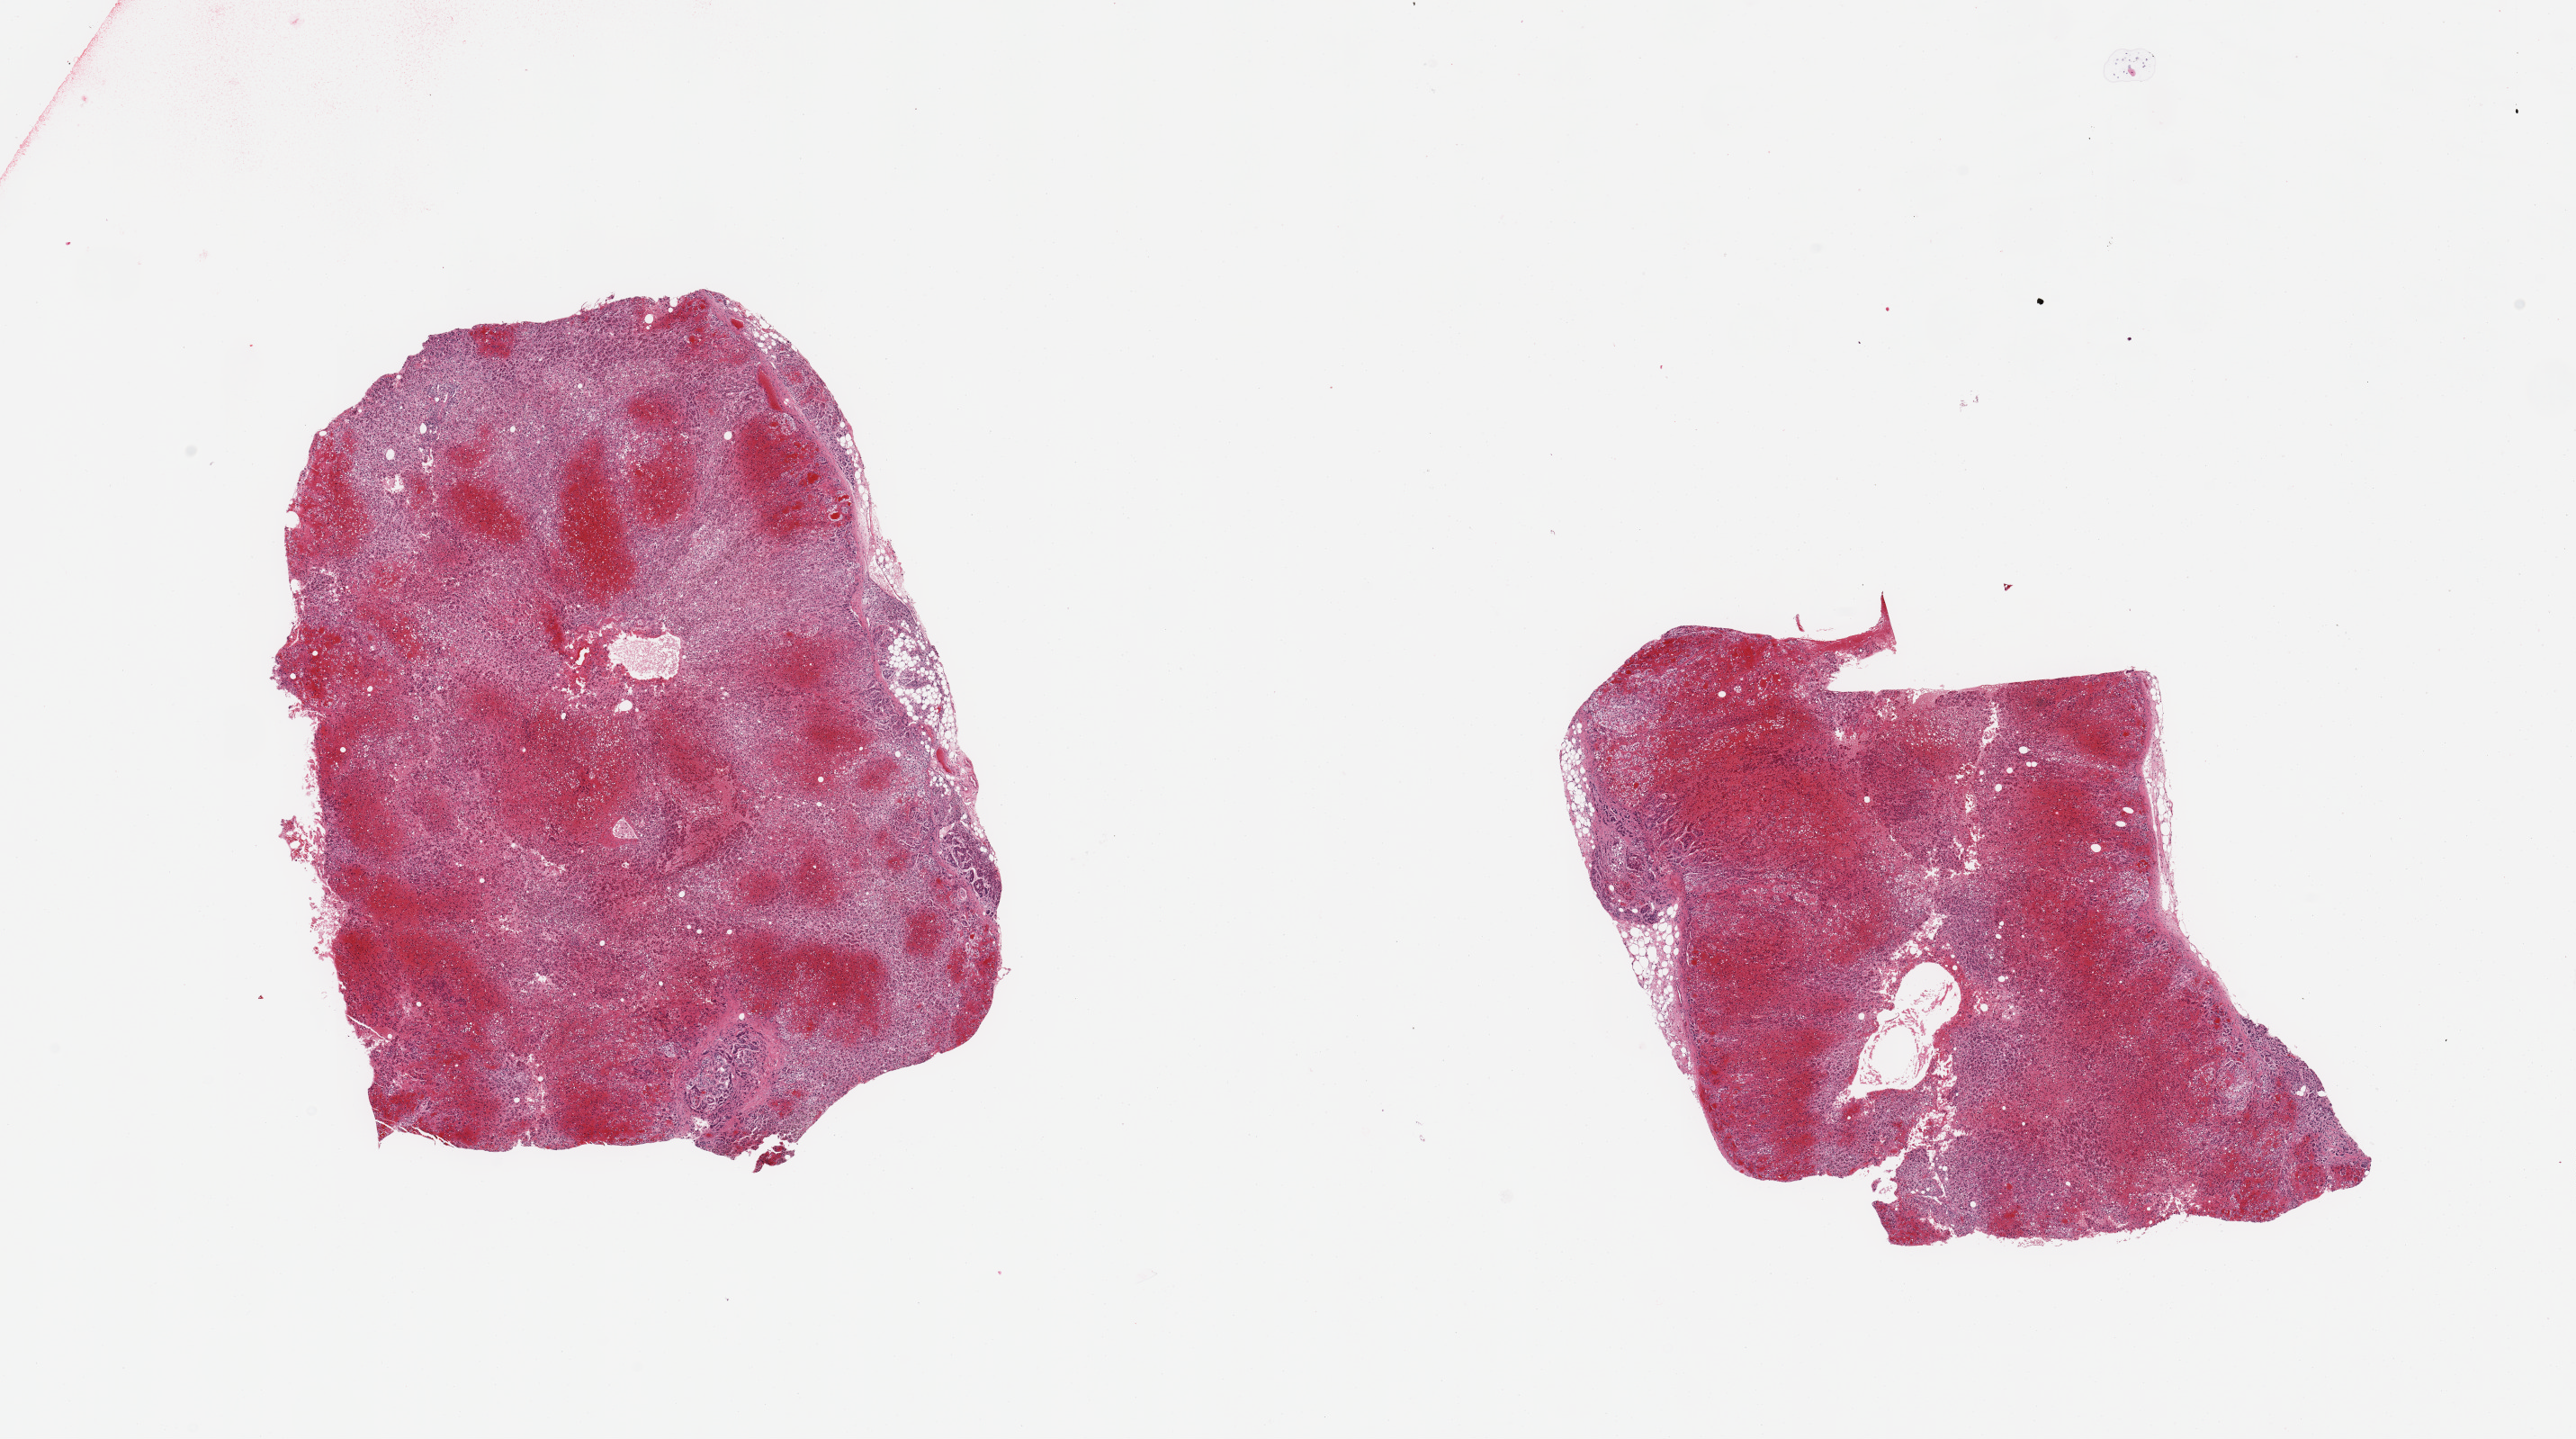
Digitized H&E-stained section, brightfield — low-resolution overview of the scanned area, about 22.6 x 12.6 mm (slide scanned at 20x), PAXgene-fixed paraffin-embedded (PFPE) section, target tissue: adrenal gland, tissue donor sample. Donor sex: male.
- reviewer comment on this tissue sample: 2 pieces; numerous hemorrhages in 60% area